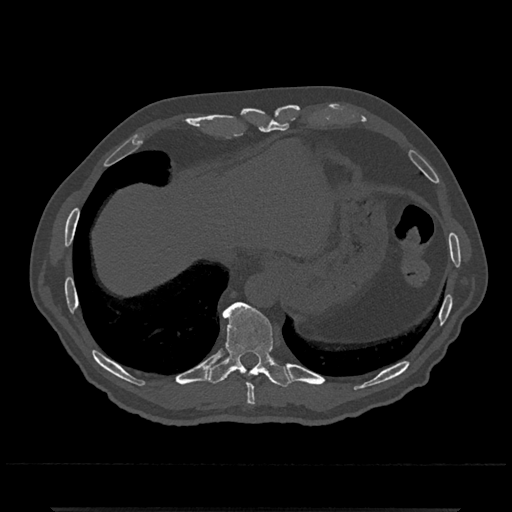
CT including the spine, one axial slice; position 569 of 797 along the scan axis; reconstruction kernel Br40s/3; 120 kVp; bone window (W 1800 / L 400 HU); 512 × 512 image matrix, field of view 393 × 393 mm. Male patient, age 67 years. Case-level facts recorded for this patient, not image findings: primary cancer: prostate.
Structures marked on this image (semi-automatic segmentation, software-assisted and operator-edited):
- T10 vertebra: bounding box <206,302,292,388> (left, top, right, bottom; pixels)
- T9 vertebra: <246,383,256,406>